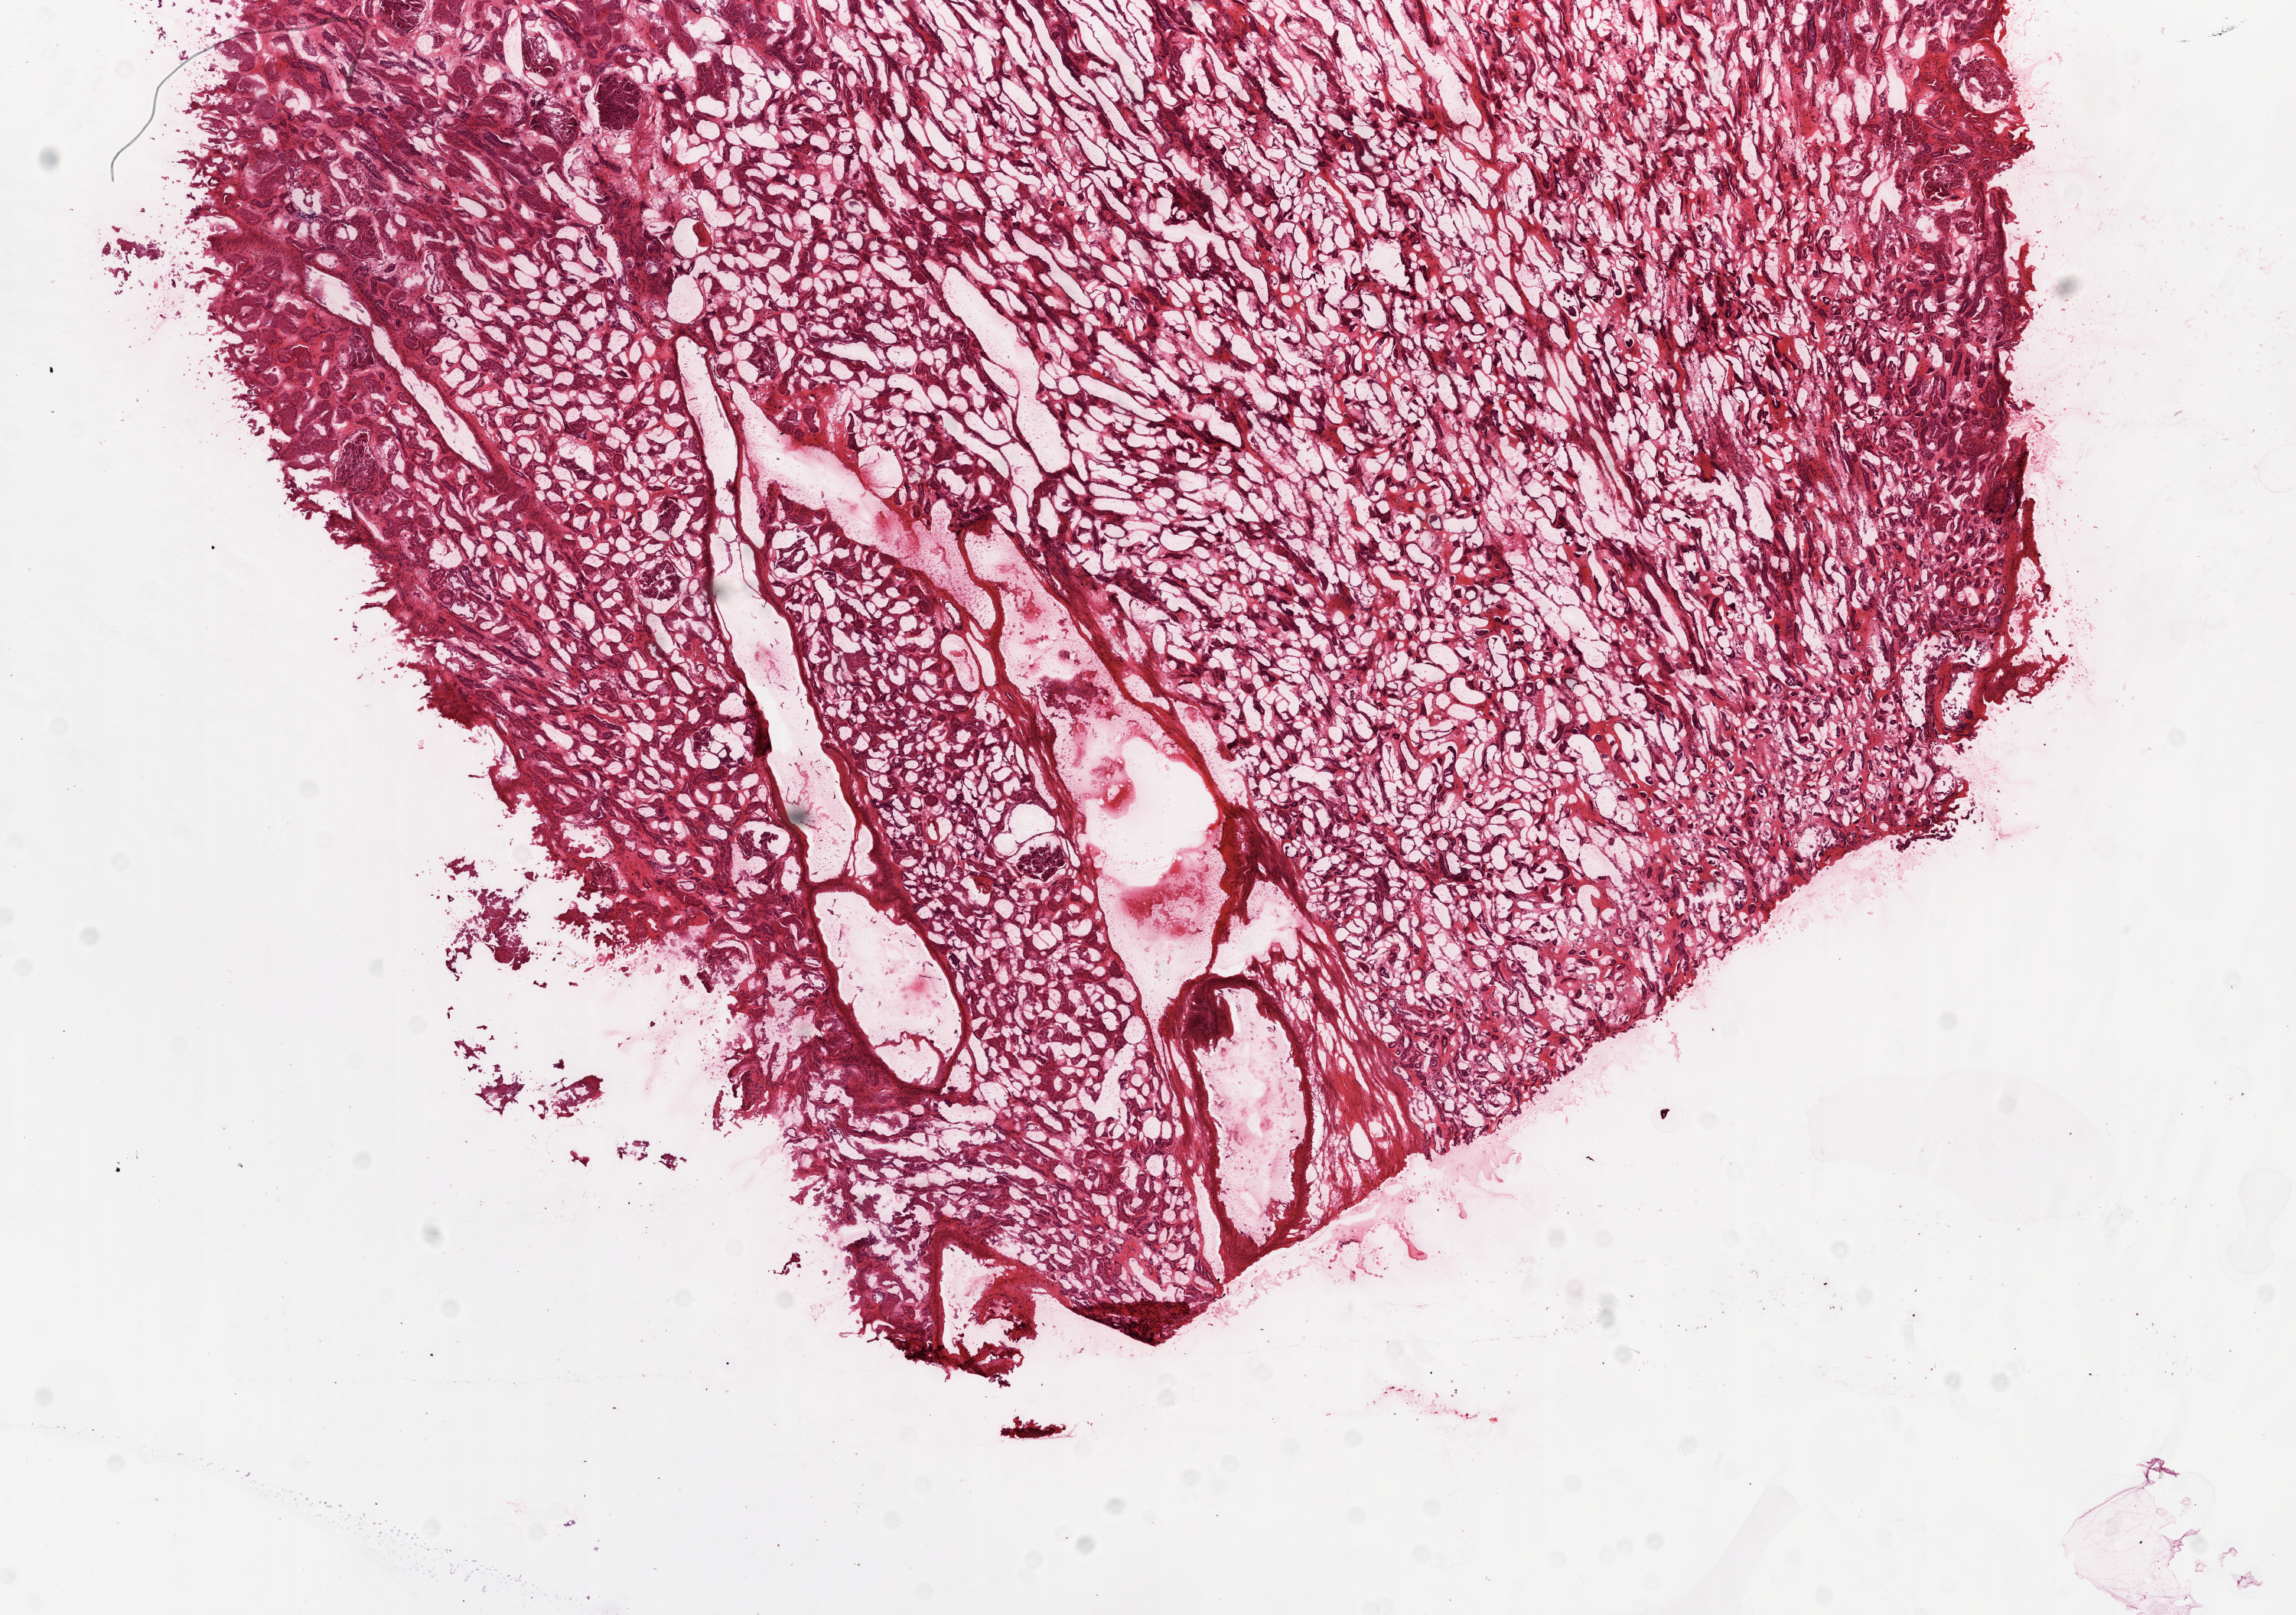
Digitized Hematoxylin and eosin (H&E) stained tissue section (whole slide), whole scanned area (about 11.9 x 8.4 mm) shown as a low-resolution overview, frozen section from the top of the tissue portion, solid tissue normal (non-tumour tissue) sample from the kidney. Patient: male, age at initial diagnosis 57 years.
This section: solid tissue normal (non-tumour) sample from the same patient. Patient diagnosis: Clear cell adenocarcinoma, NOS.